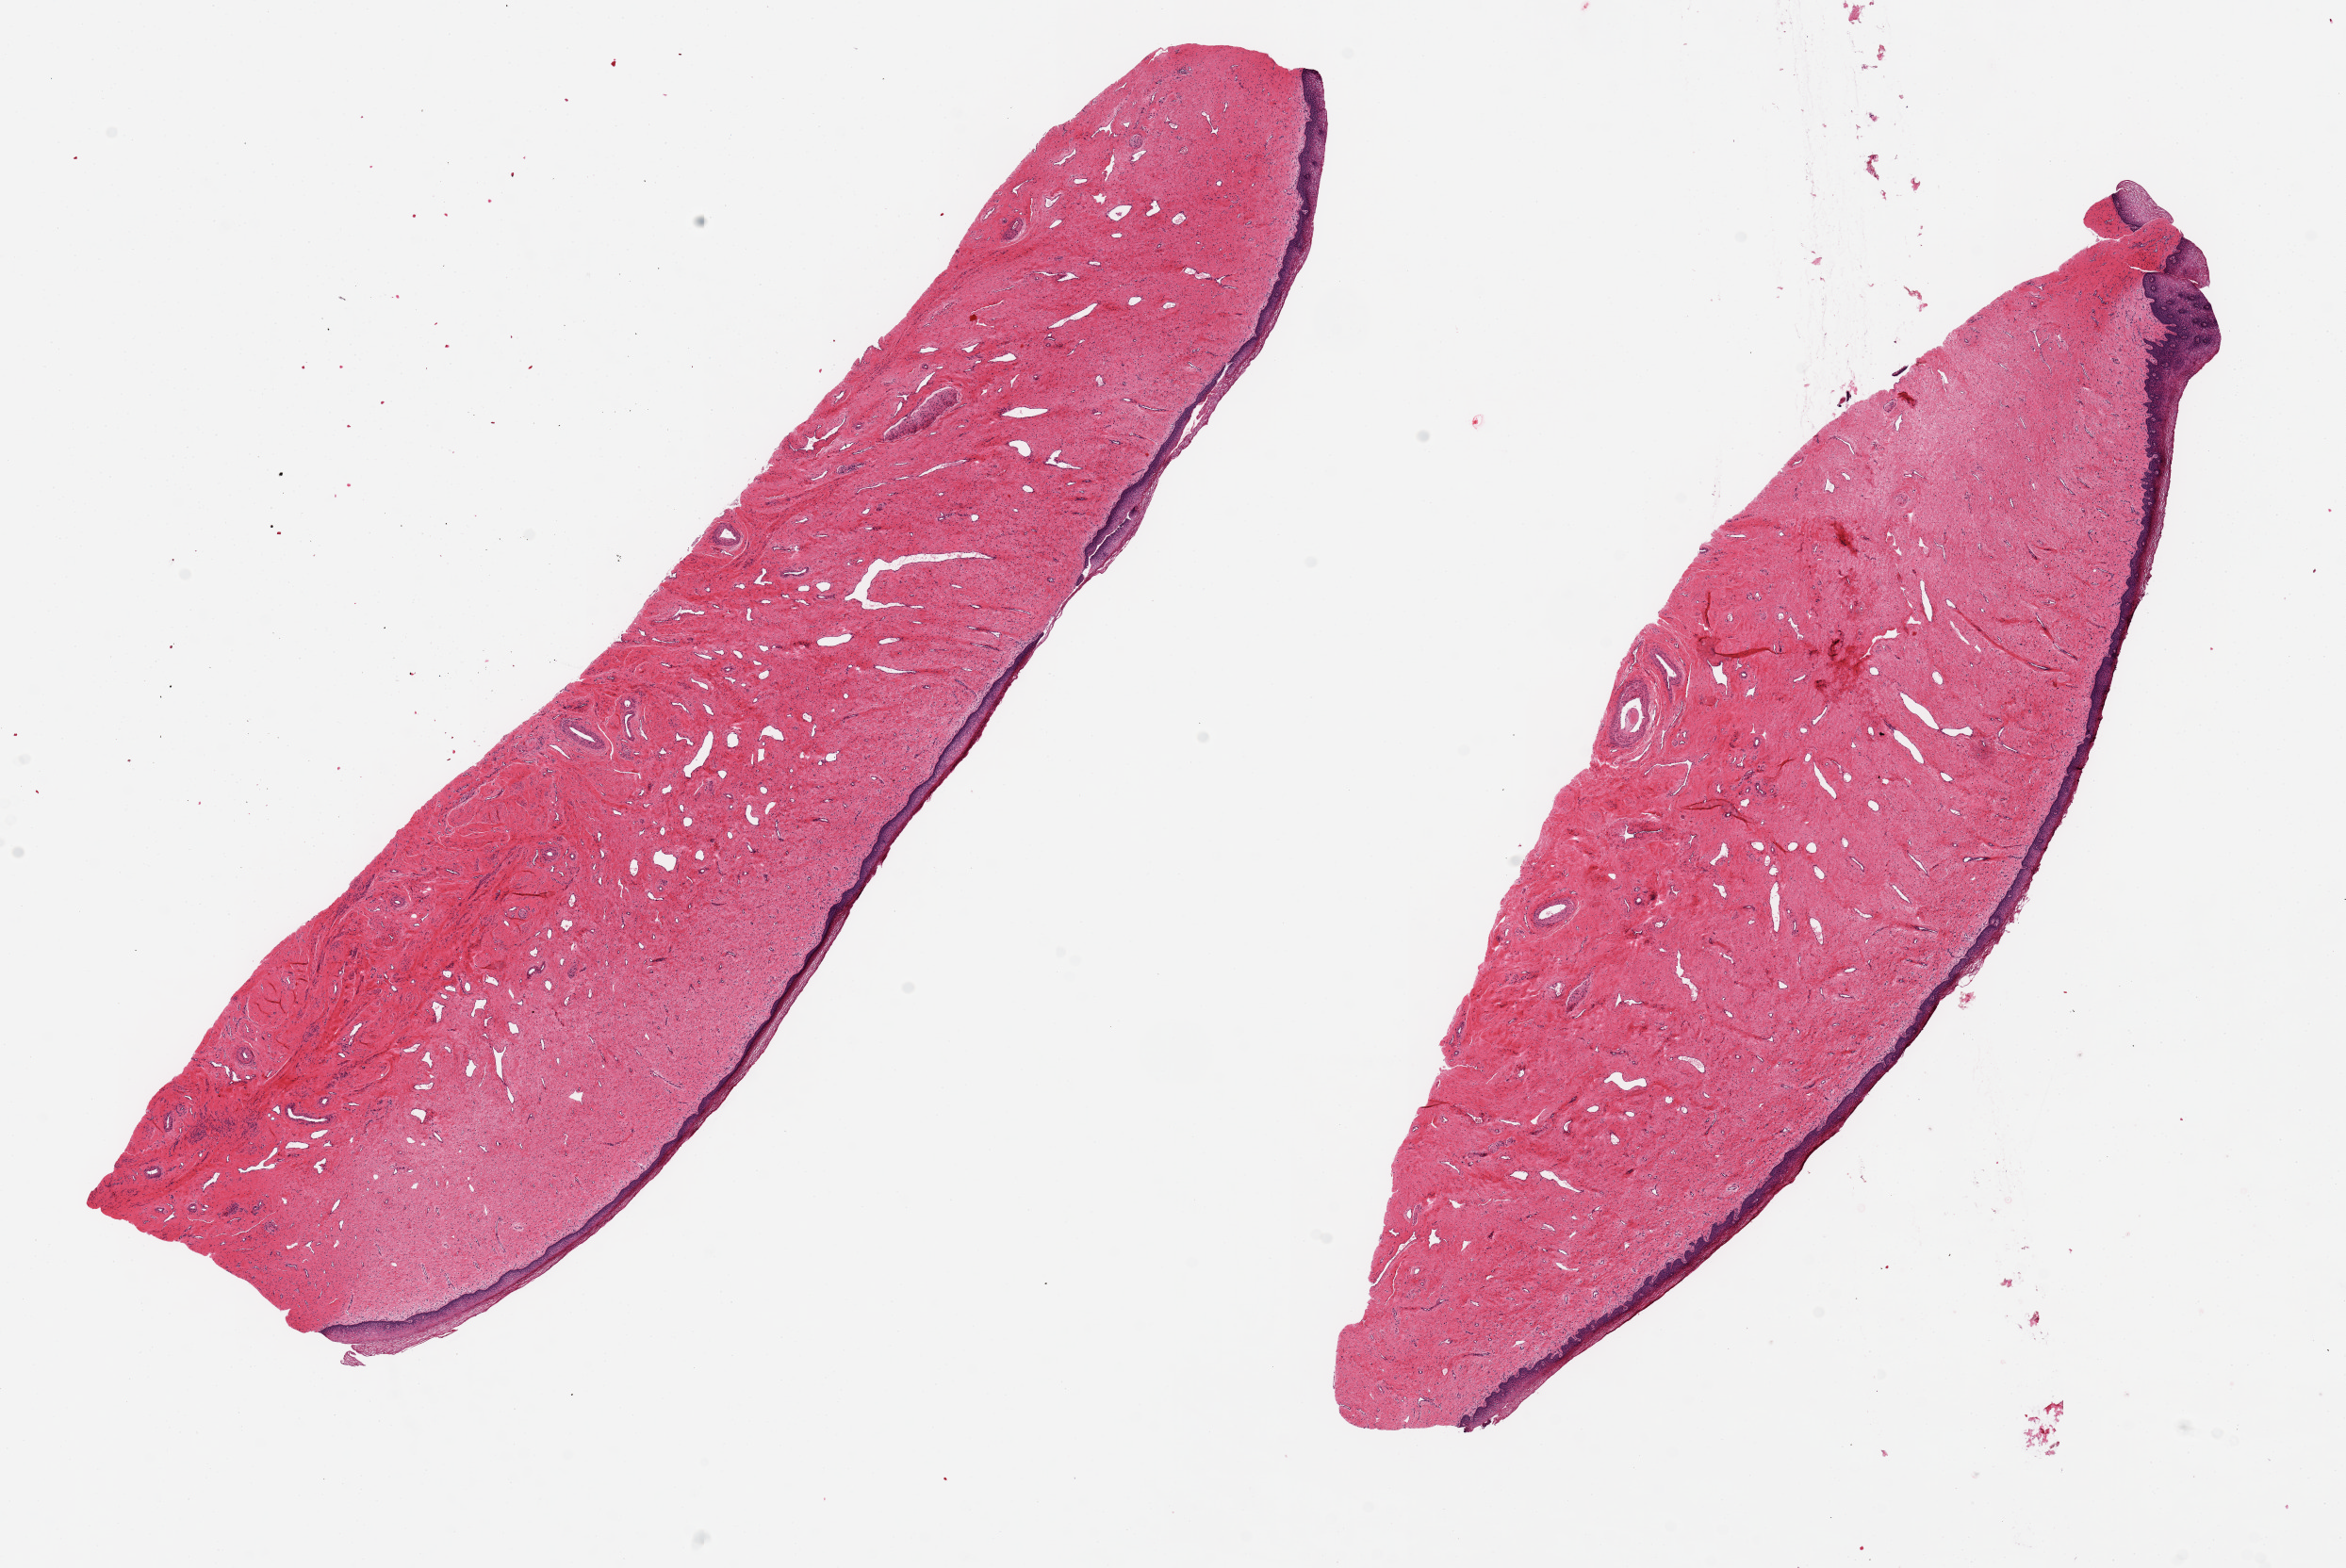
Whole-slide image, H&E stain — whole scanned area (about 19.7 x 13.2 mm) shown as a low-resolution overview. PAXgene-fixed paraffin-embedded (PFPE) section. Sampled site (target tissue): exocervix. Tissue donor sample. Donor sex: female.
Pathologist's review note for this sample: 2 aliquots ~ 12.5x3mm. Squamous mucosa (keratinizing in foci) is 3-5% of thickness; good specimens.